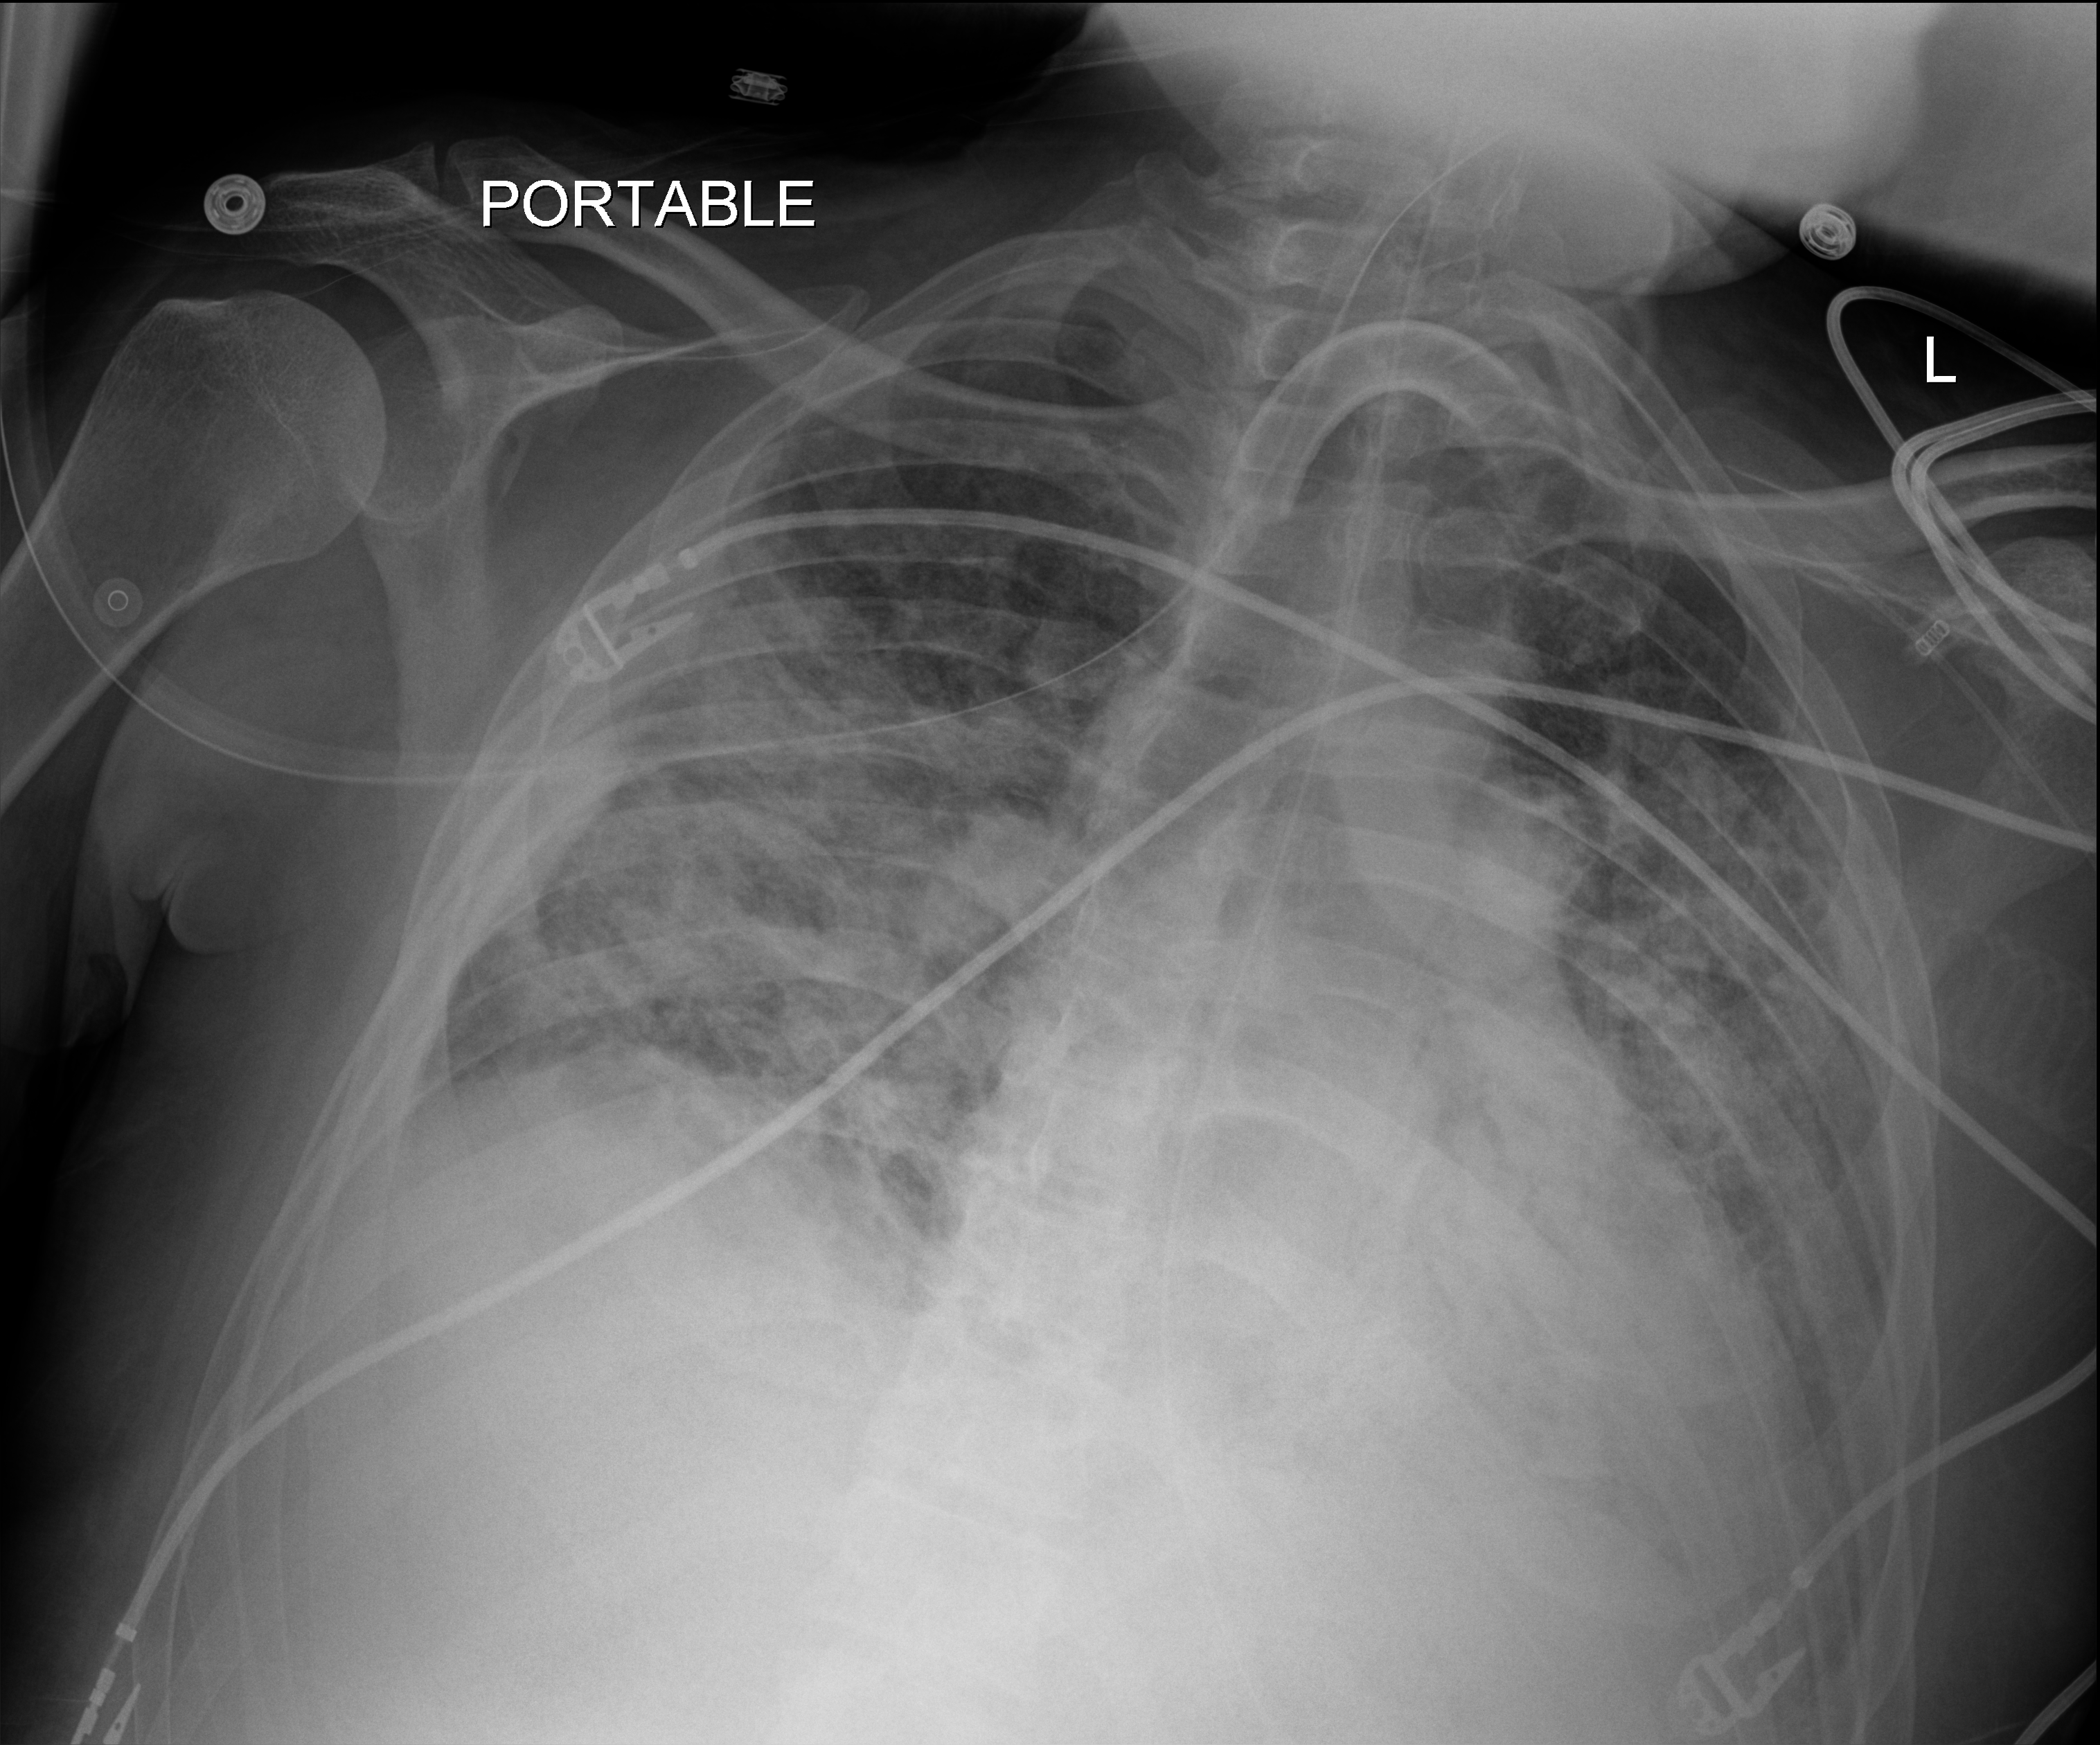
Chest X-ray (portable). Male patient hospitalised with COVID-19, age 18–59 years.
Hospital-stay facts (about this admission, not read from this image; timing relative to this image not recorded):
- admitted to intensive care during this hospital stay: yes
- mechanically ventilated during this hospital stay: yes